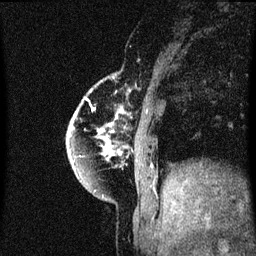
Breast MRI (dynamic contrast-enhanced), one sagittal slice. Position 11 of 60 along the scan axis. Dynamic contrast-enhanced series, image 2 of 3 at this slice position (ordered by acquisition). 1.5 T. TE 4.2 ms, TR 8.4 ms. 2 mm slice thickness. 256 × 256 image matrix, field of view 200 × 200 mm. Patient: female, 60 years.
Structures marked on this image (semi-automatic segmentation, software-assisted and operator-edited):
- analysis volume of interest (the breast-tissue region the enhancement analysis was run in; not a lesion): bounding box [x1, y1, x2, y2] px = [66, 84, 125, 195]
- tumour enhancement mask (voxels above the 70 % enhancement threshold inside the analysis volume of interest): [68, 98, 119, 167]